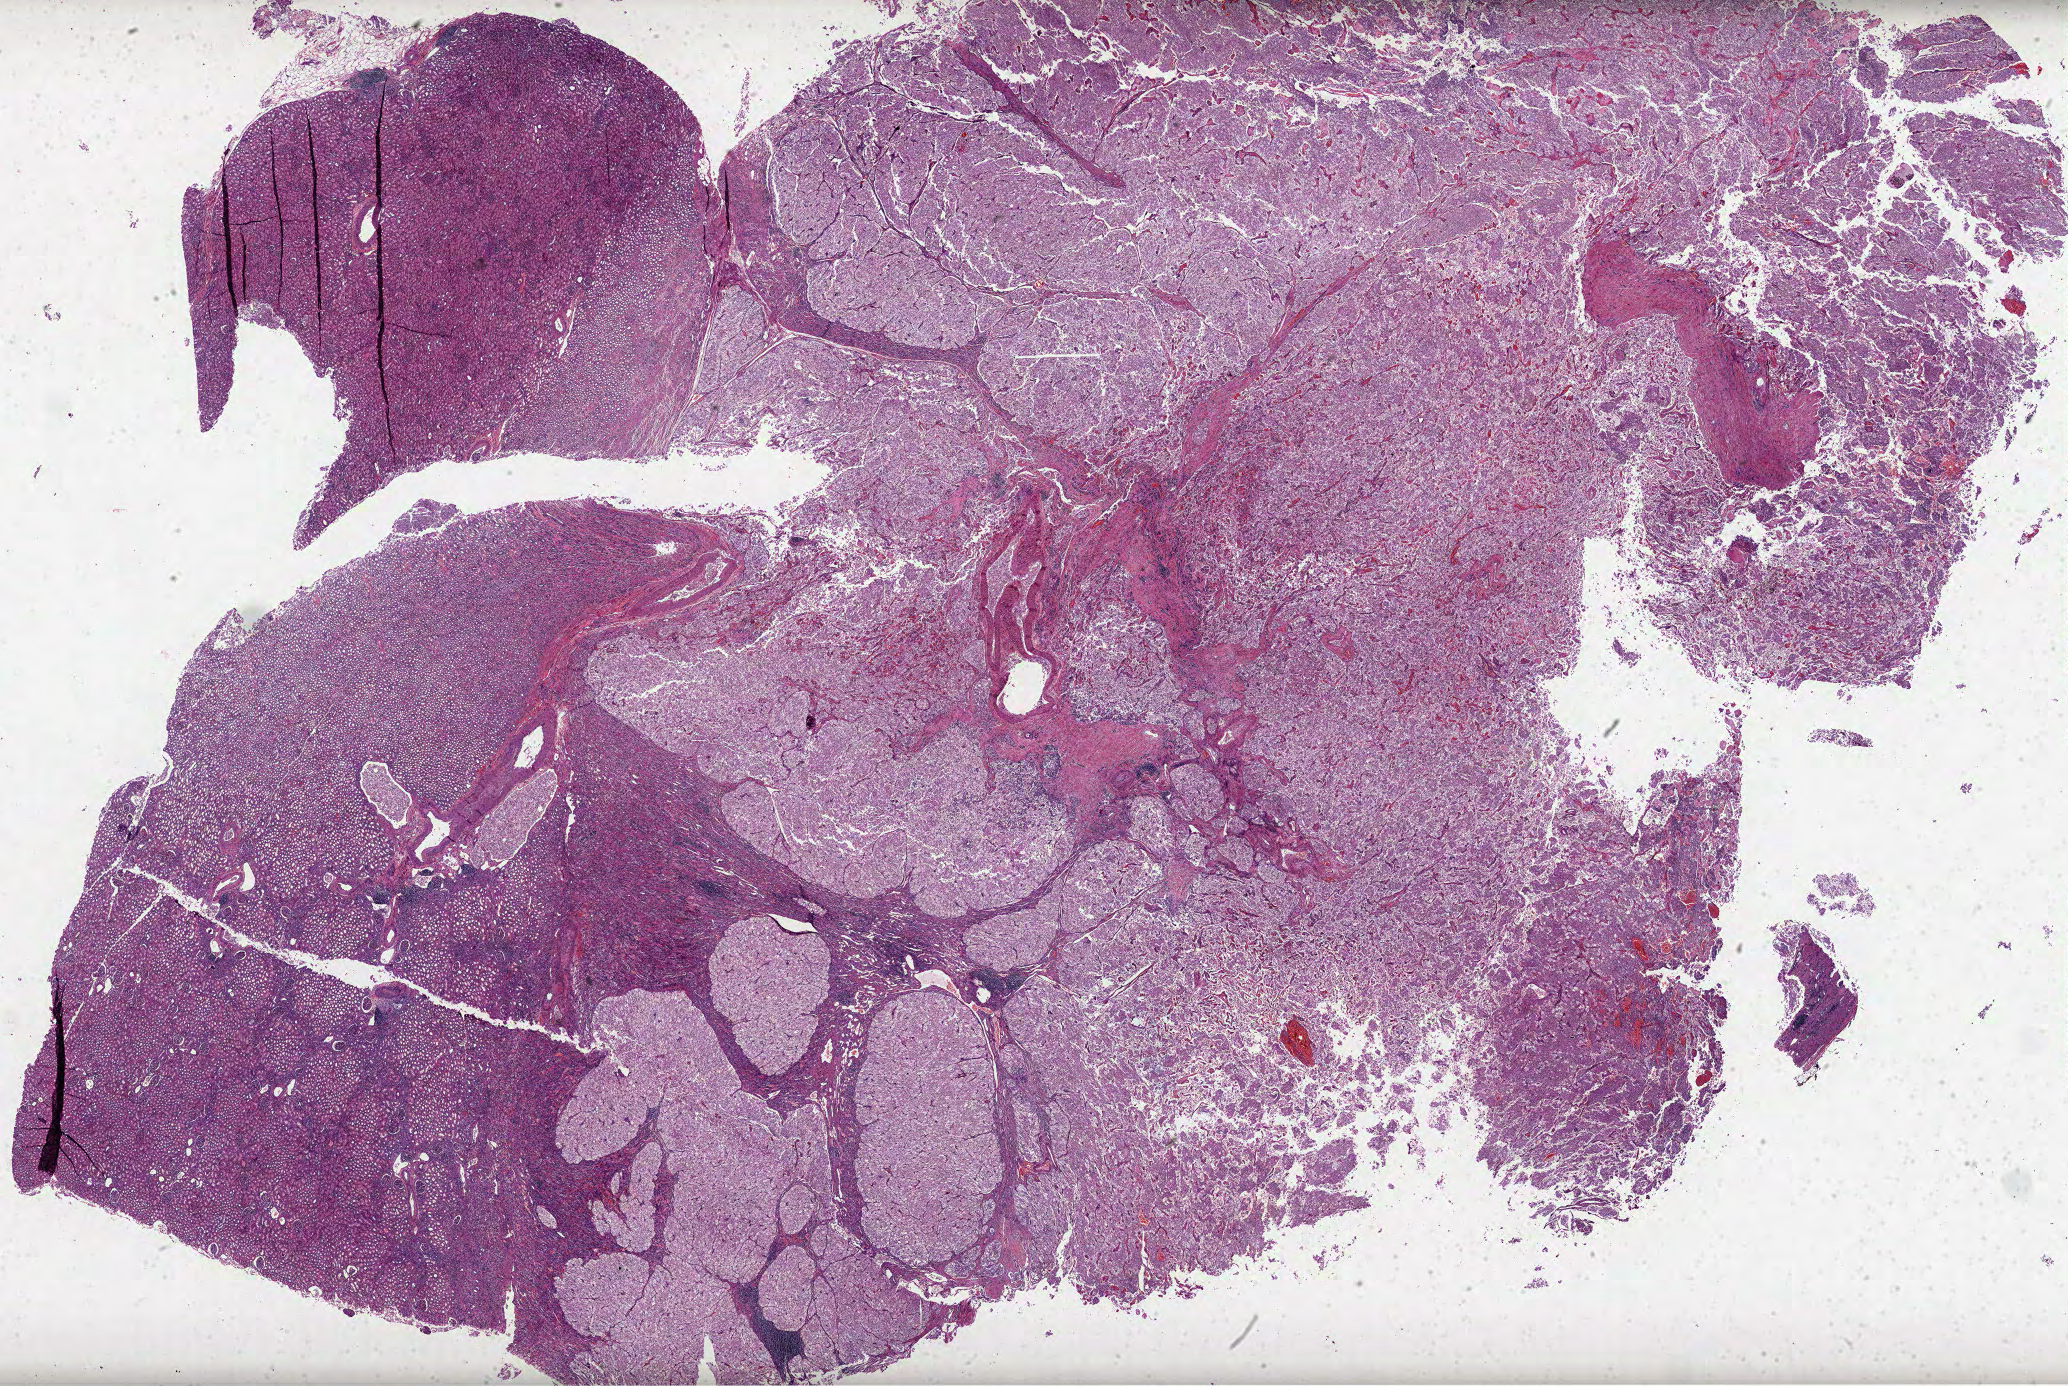
Digitized Hematoxylin and eosin (H&E) stained tissue section (whole slide), low-resolution overview of the scanned area, about 33.4 x 22.4 mm (slide scanned at 40x), FFPE section, primary tumour sample from the kidney. Patient: male, age at initial diagnosis 40 years. Histologic grade: G2 (moderately differentiated).
• pathologic diagnosis: Clear cell adenocarcinoma, NOS
• AJCC pathologic stage: I
• laterality: right